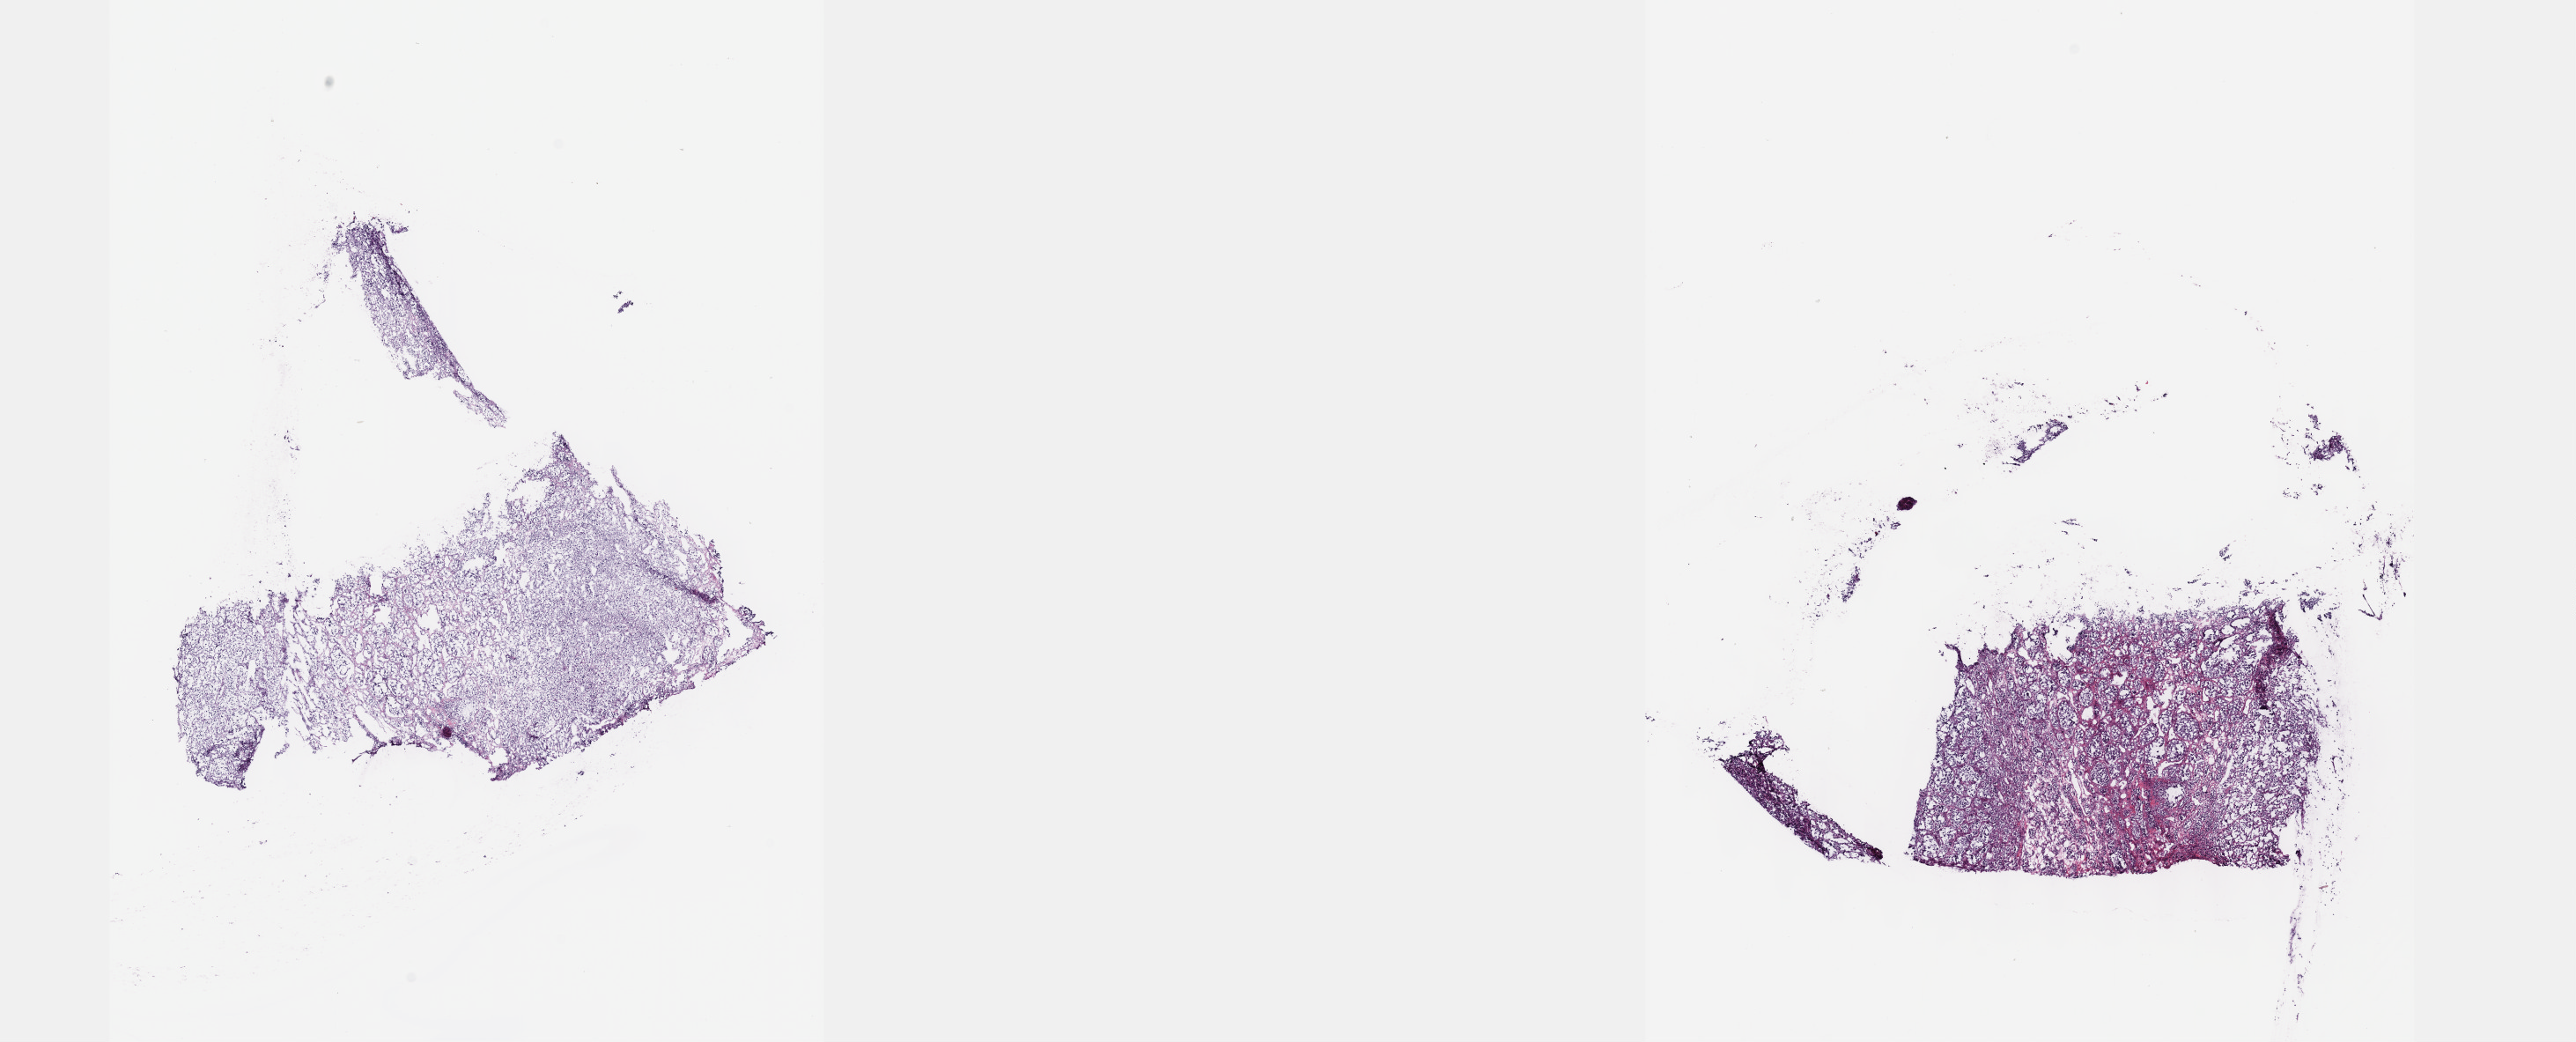
Digitized Hematoxylin and eosin (H&E) stained tissue section (whole slide) — low-resolution overview of the scanned area, about 23.6 x 9.6 mm (acquisition: 40x scan); frozen section from the top of the tissue portion; sample: primary tumour, adrenal gland. Male patient; age at initial diagnosis 23 years. Slide review estimates, as recorded: tumour cells 90%, tumour nuclei 90%, normal cells 0%, stromal cells 10%, necrosis 0%. Infiltration values recorded for this section: lymphocyte infiltration 40%, monocyte infiltration 20%, neutrophil infiltration 20%.
Histologic diagnosis: Clear cell carcinoma (kidney, NOS).